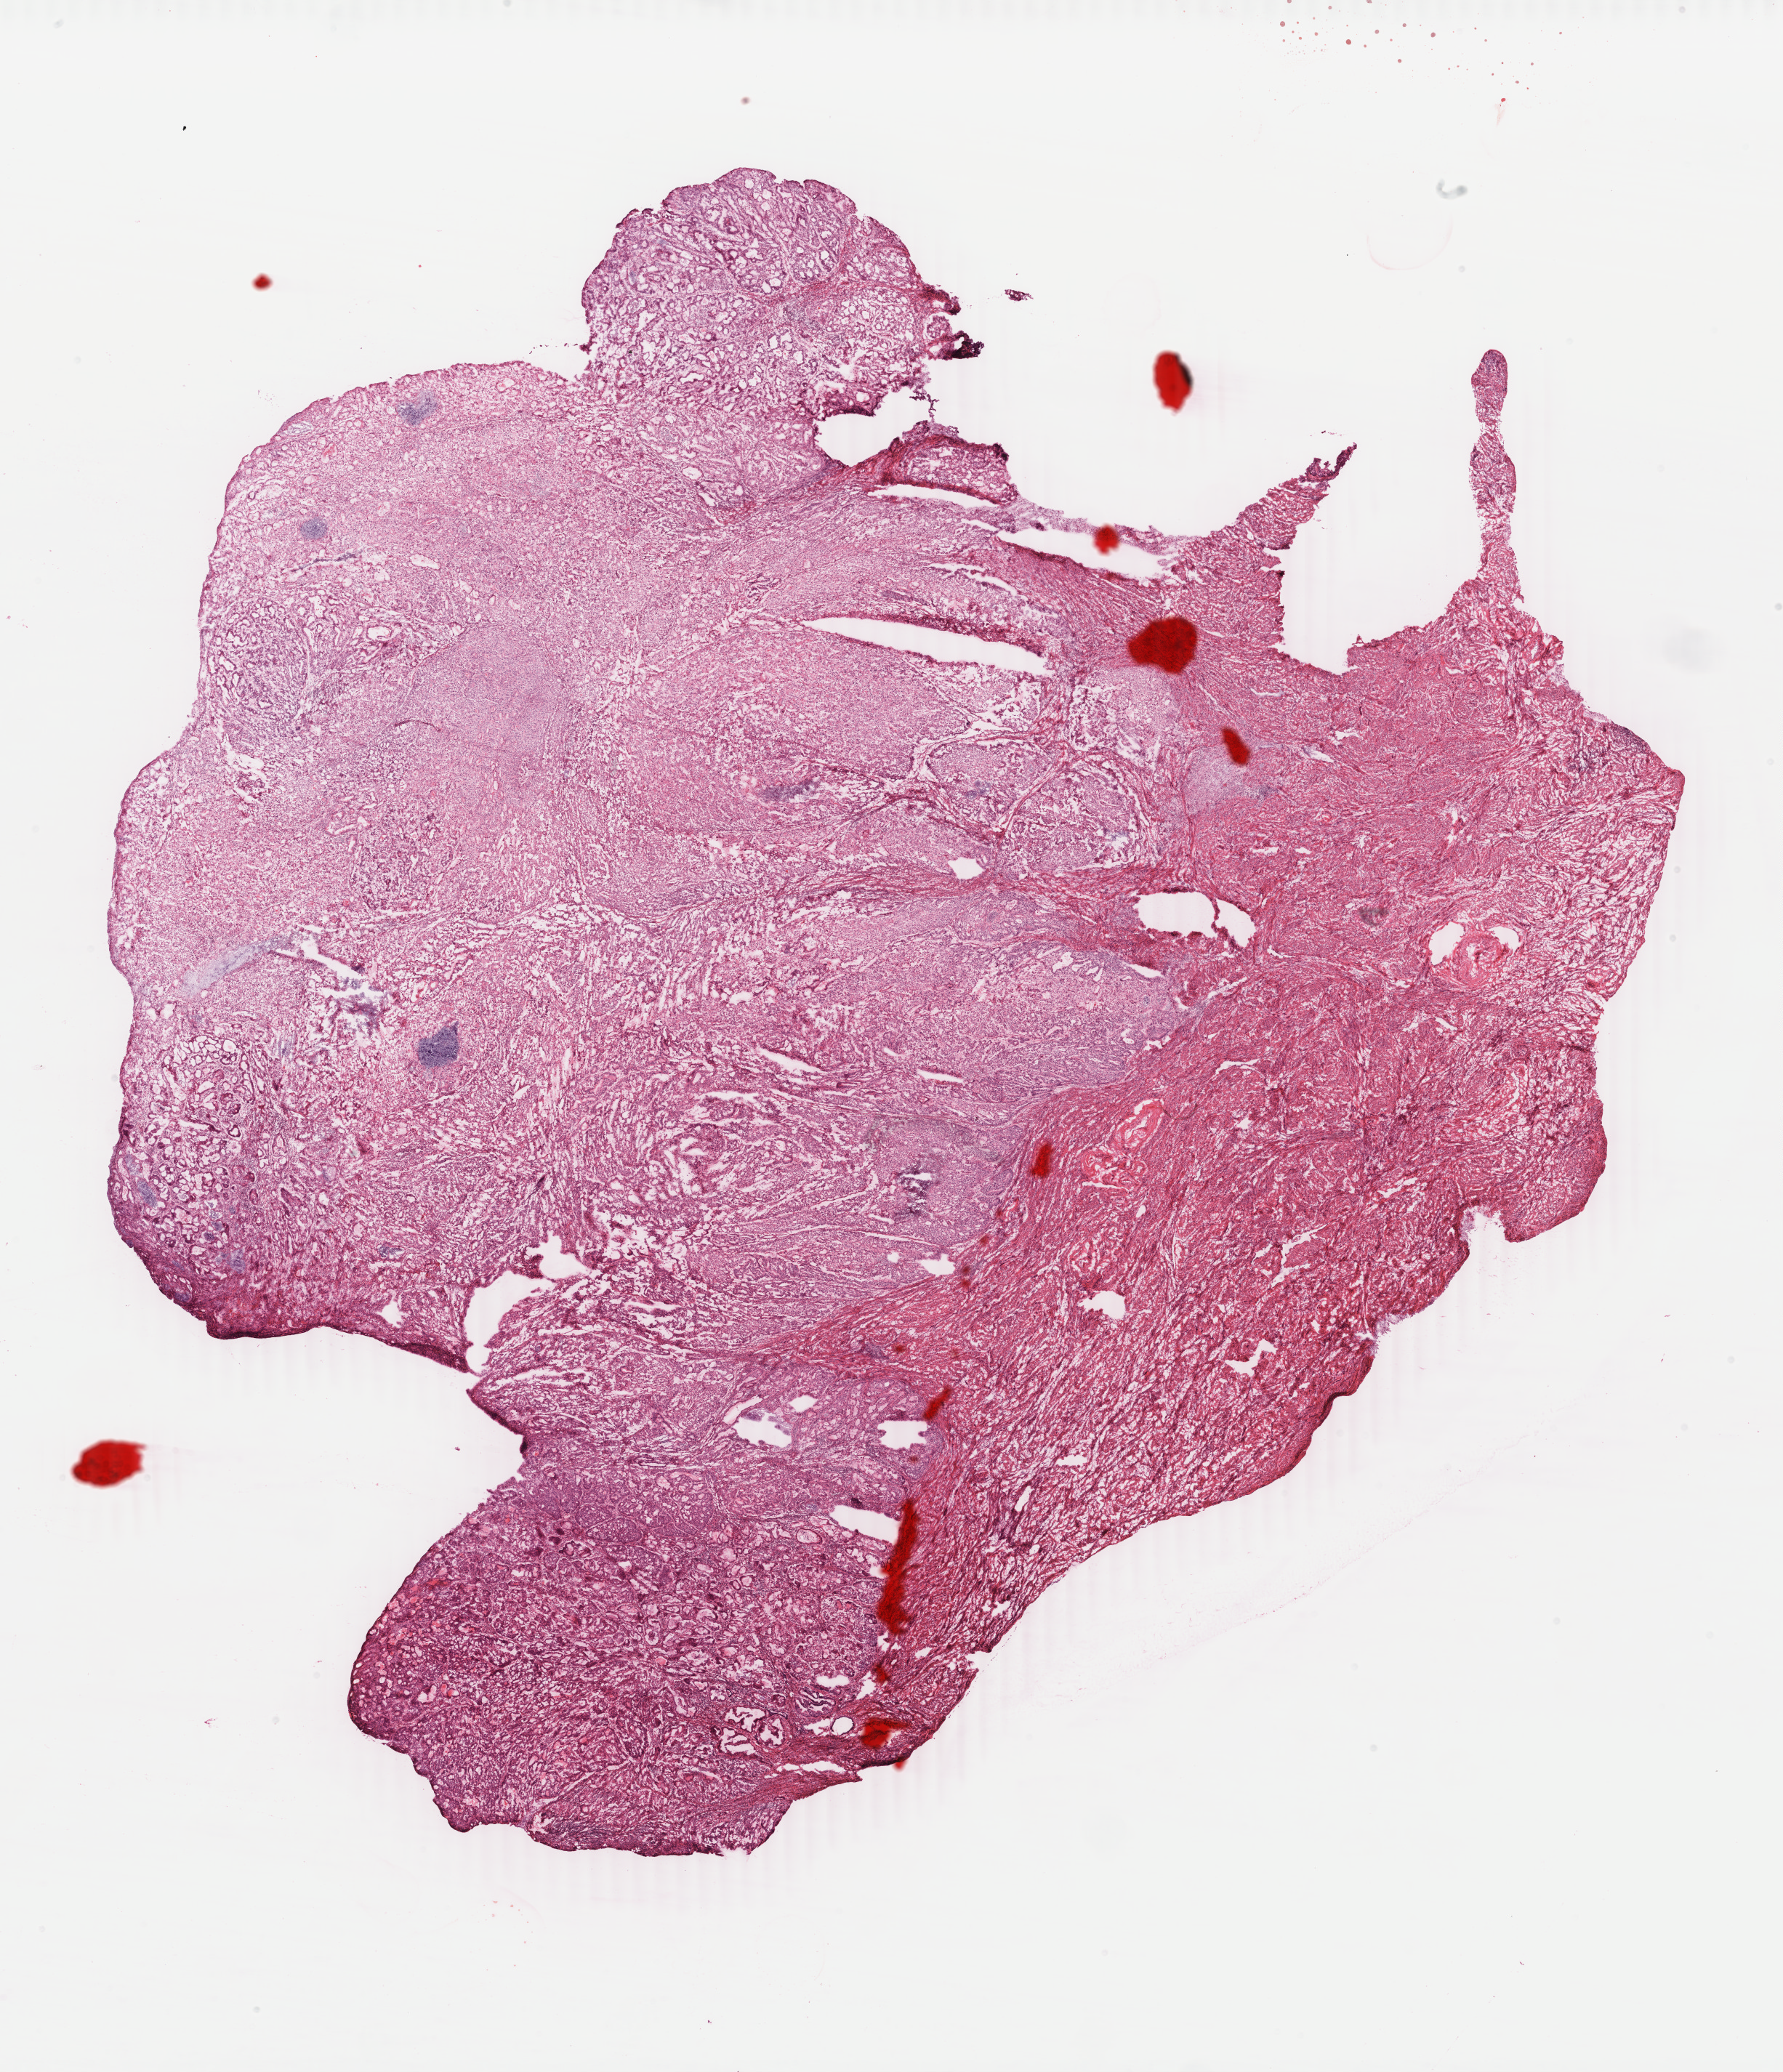
Whole-slide histology image, H&E, whole scanned area (about 19.5 x 22.7 mm, slide scanned at 40x) shown as a low-resolution overview. FFPE section. Sample: primary tumour, uterus. Patient: female, age at initial diagnosis 73 years. Histologic grade: G2 (moderately differentiated).
Histologic diagnosis: Endometrioid adenocarcinoma, NOS (endometrium). FIGO stage: IA.